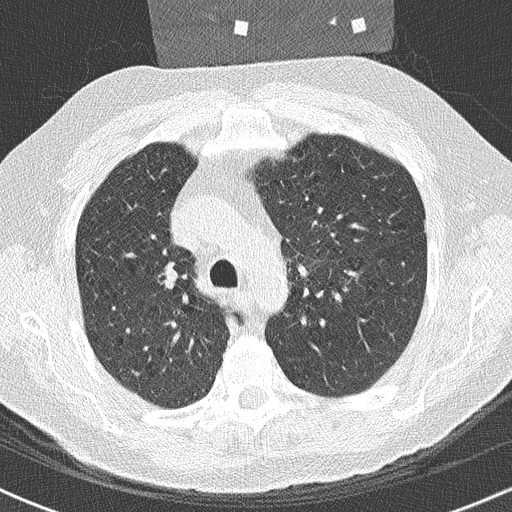
Low-dose screening chest CT, axial slice; baseline annual screen; lung window (W 1500 / L -600 HU); lung (sharp) reconstruction kernel (B50f); 512 × 512 image matrix. Male, age 59 years at enrolment.
Lesion marked by an expert reader, box from (x=147, y=257) to (x=181, y=294) px. Screening reader's record for this exam: no non-calcified nodule ≥4 mm recorded. Official screen result: negative screen, minor abnormalities not suspicious for lung cancer. Participant outcome: lung cancer diagnosed 360 days after this screen — squamous cell carcinoma, NOS, right upper lobe, poorly differentiated (G3), stage IIA (AJCC 6th edition), 20 mm at pathology.